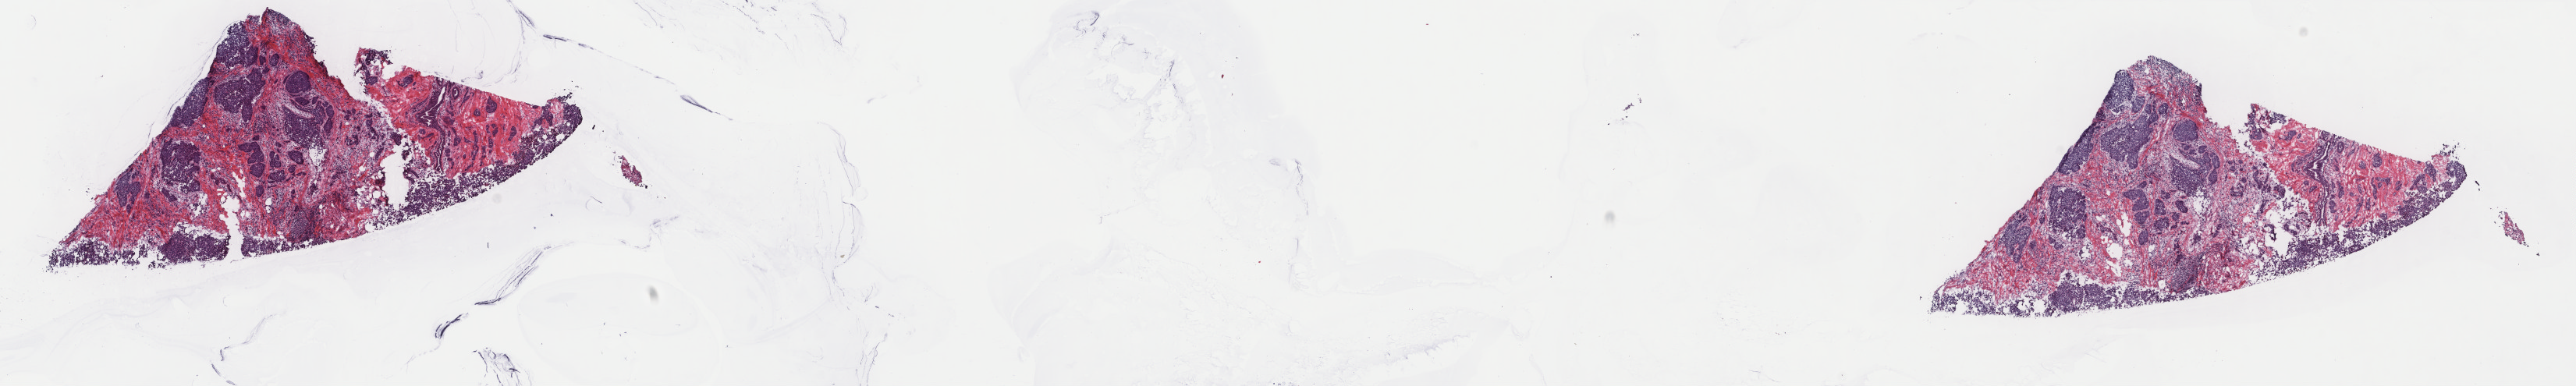
Digitized H&E-stained tissue section (whole slide) — whole scanned area (about 26.2 x 3.9 mm, acquisition: 40x scan) shown as a low-resolution overview; frozen section from the top of the tissue portion; sample: primary tumour, breast. Female patient; age at initial diagnosis 74 years. Composition of this section per pathologist review: tumour cells 80%, tumour nuclei 65%.
Histologic diagnosis: Infiltrating duct carcinoma, NOS.